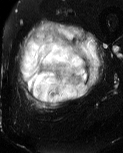
MRI of an extremity soft-tissue mass, one axial slice. Position 19 of 60 along the scan axis. T2-weighted fat-saturated. MR volume resampled by the dataset authors to the PET/CT grid (not the native acquisition matrix). 3.27 mm slice thickness. 123 × 153 image matrix, field of view 120 × 149 mm. Male patient. From the clinical record (not read from this slice): histological type: pleiomorphic liposarcoma; grade: high; site of the primary tumour: left thigh.
Structures marked on this image (expert contour drawn on MRI and transferred to this co-registered scan by the dataset authors):
- gross tumour volume including surrounding oedema: bounding box <18,20,105,110> (left, top, right, bottom; pixels)
- gross tumour volume (mass): <24,36,91,105>